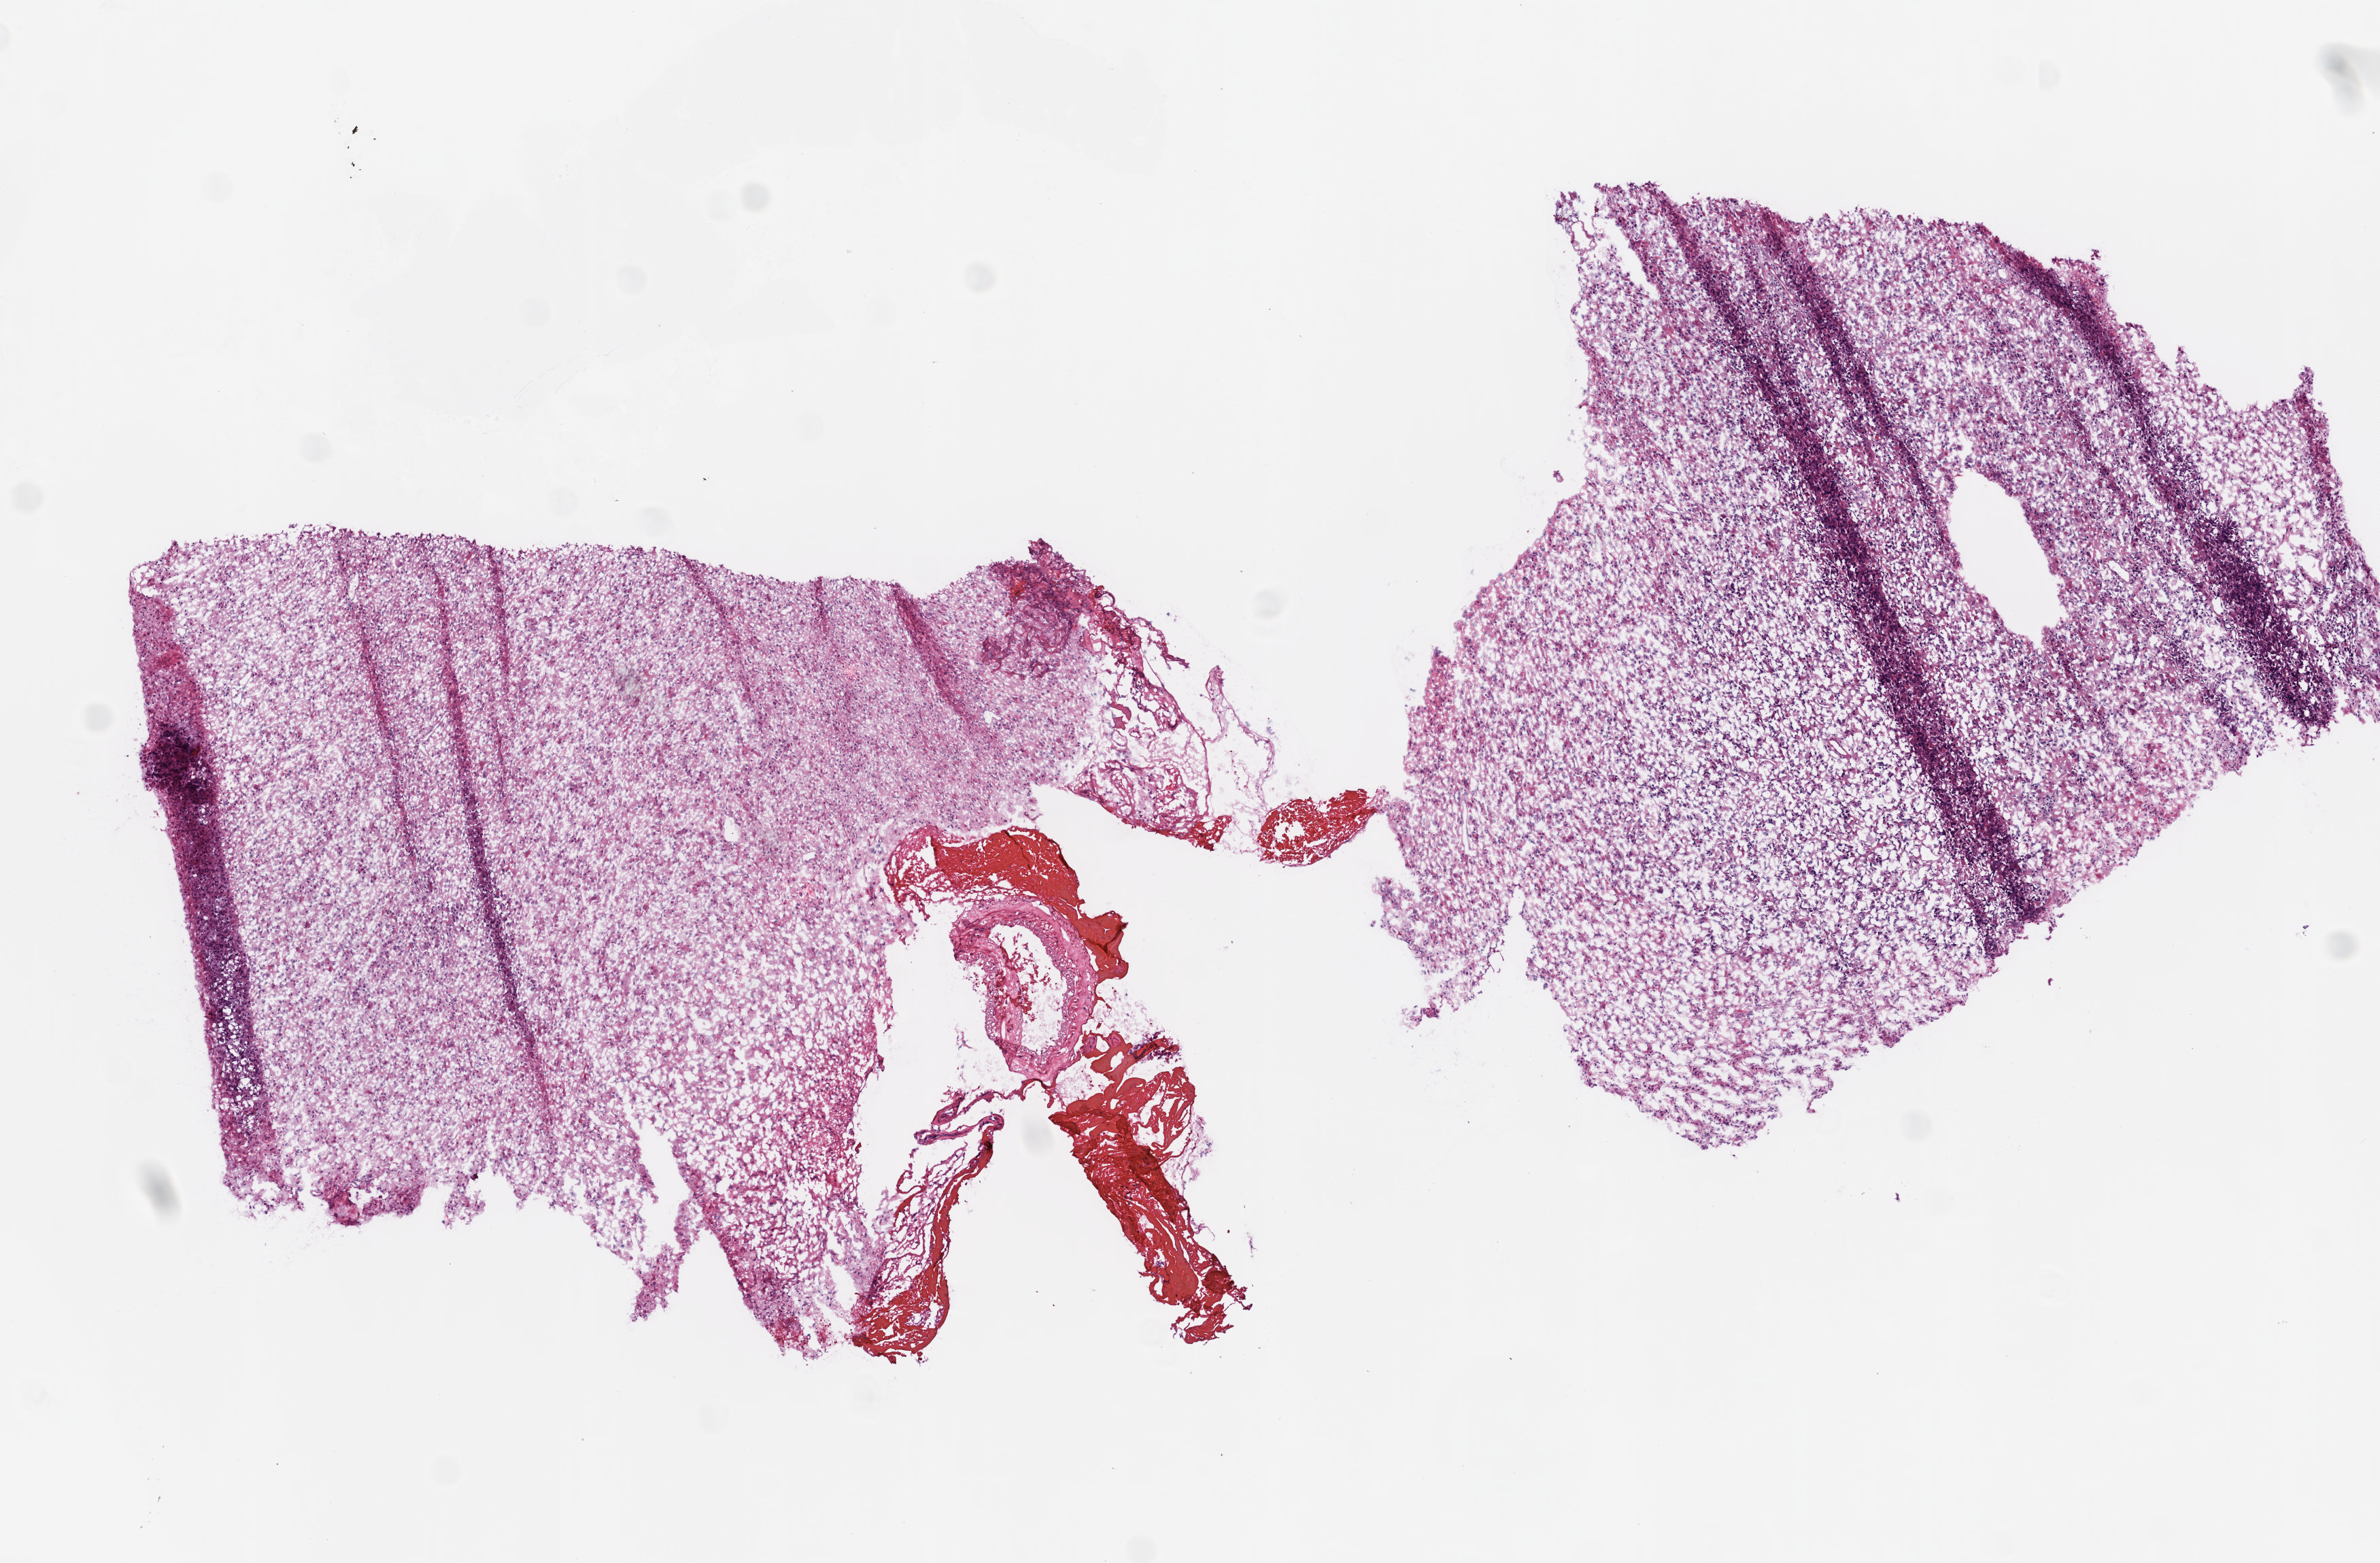
Digitized H&E-stained tissue section (whole slide) — low-resolution overview of the scanned area, about 7.0 x 4.6 mm (acquisition: 20x scan); frozen section from the bottom of the tissue portion; sample: primary tumour, brain. Male, age 80 years at initial diagnosis. Slide review estimates, as recorded: tumour cells 100%, tumour nuclei 85%, normal cells 0%, stromal cells 0%, necrosis 0%.
Diagnosis: Glioblastoma.